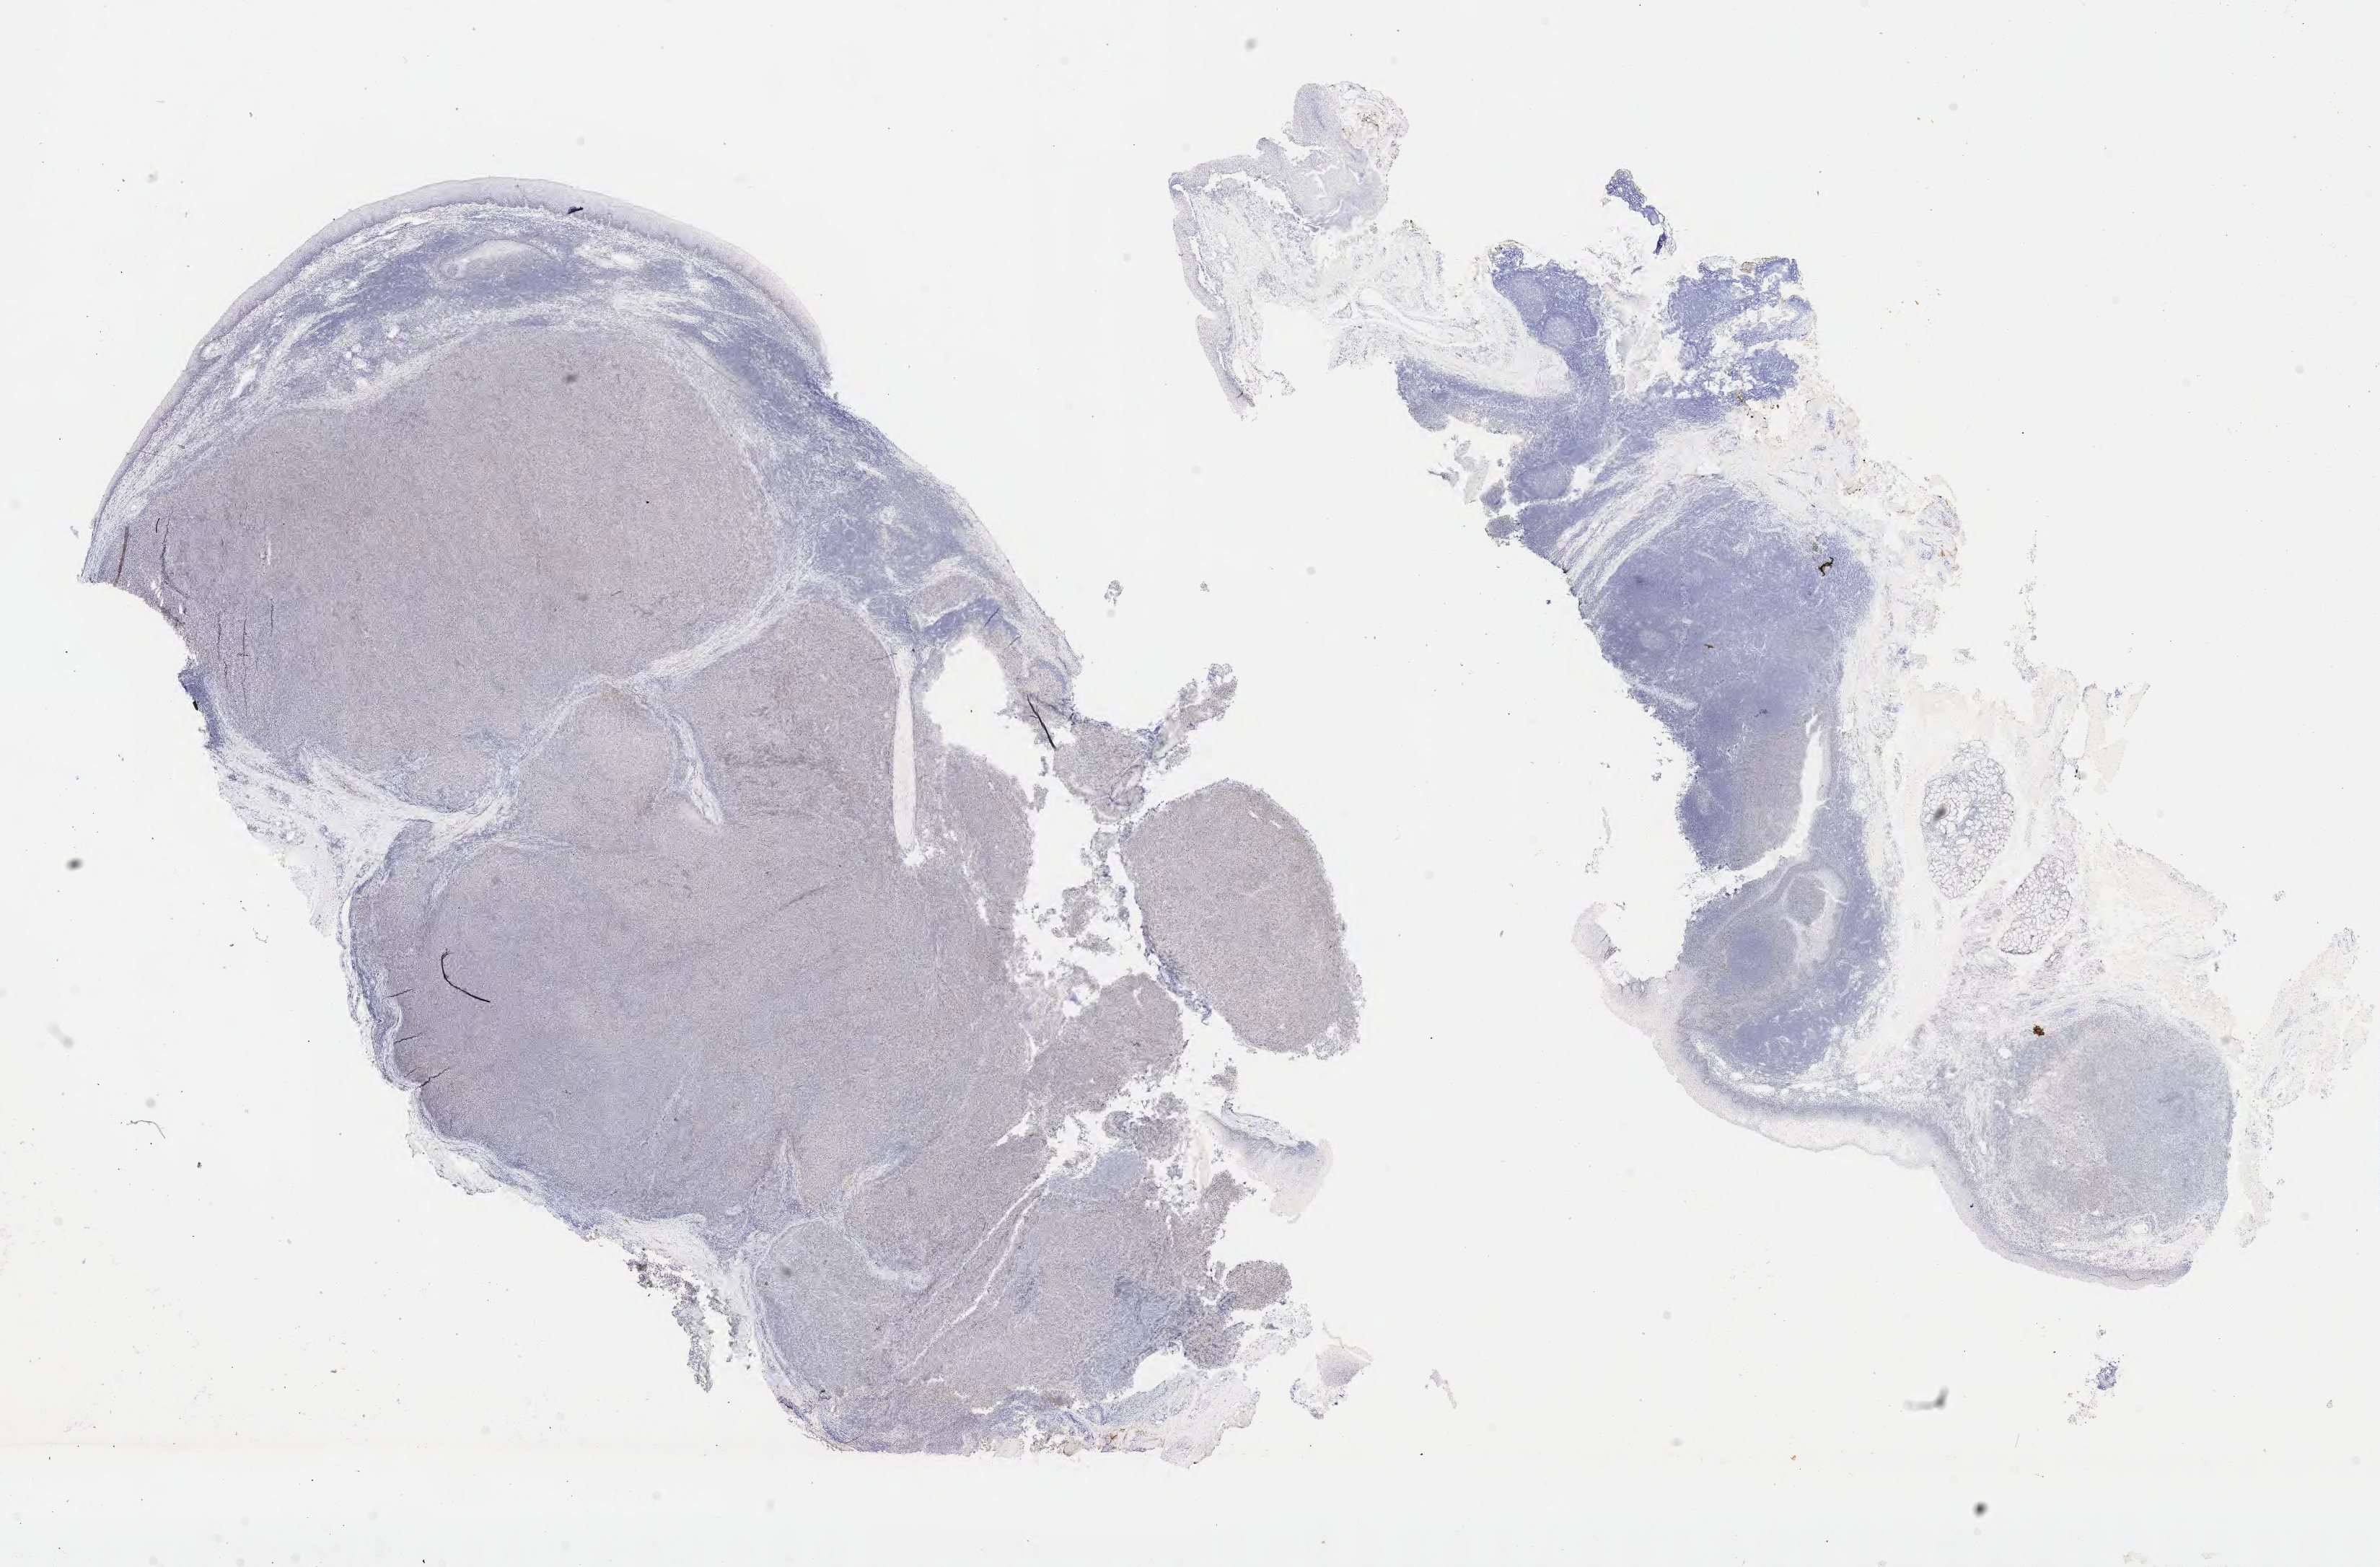
Whole-slide image, immunohistochemical stain for p53, a low-resolution overview of the entire scanned area, about 26.7 x 17.6 mm, tumor tissue, site: lymph node. Patient male; age 56 years.
Diagnosis: Diffuse large B-cell lymphoma, NOS.